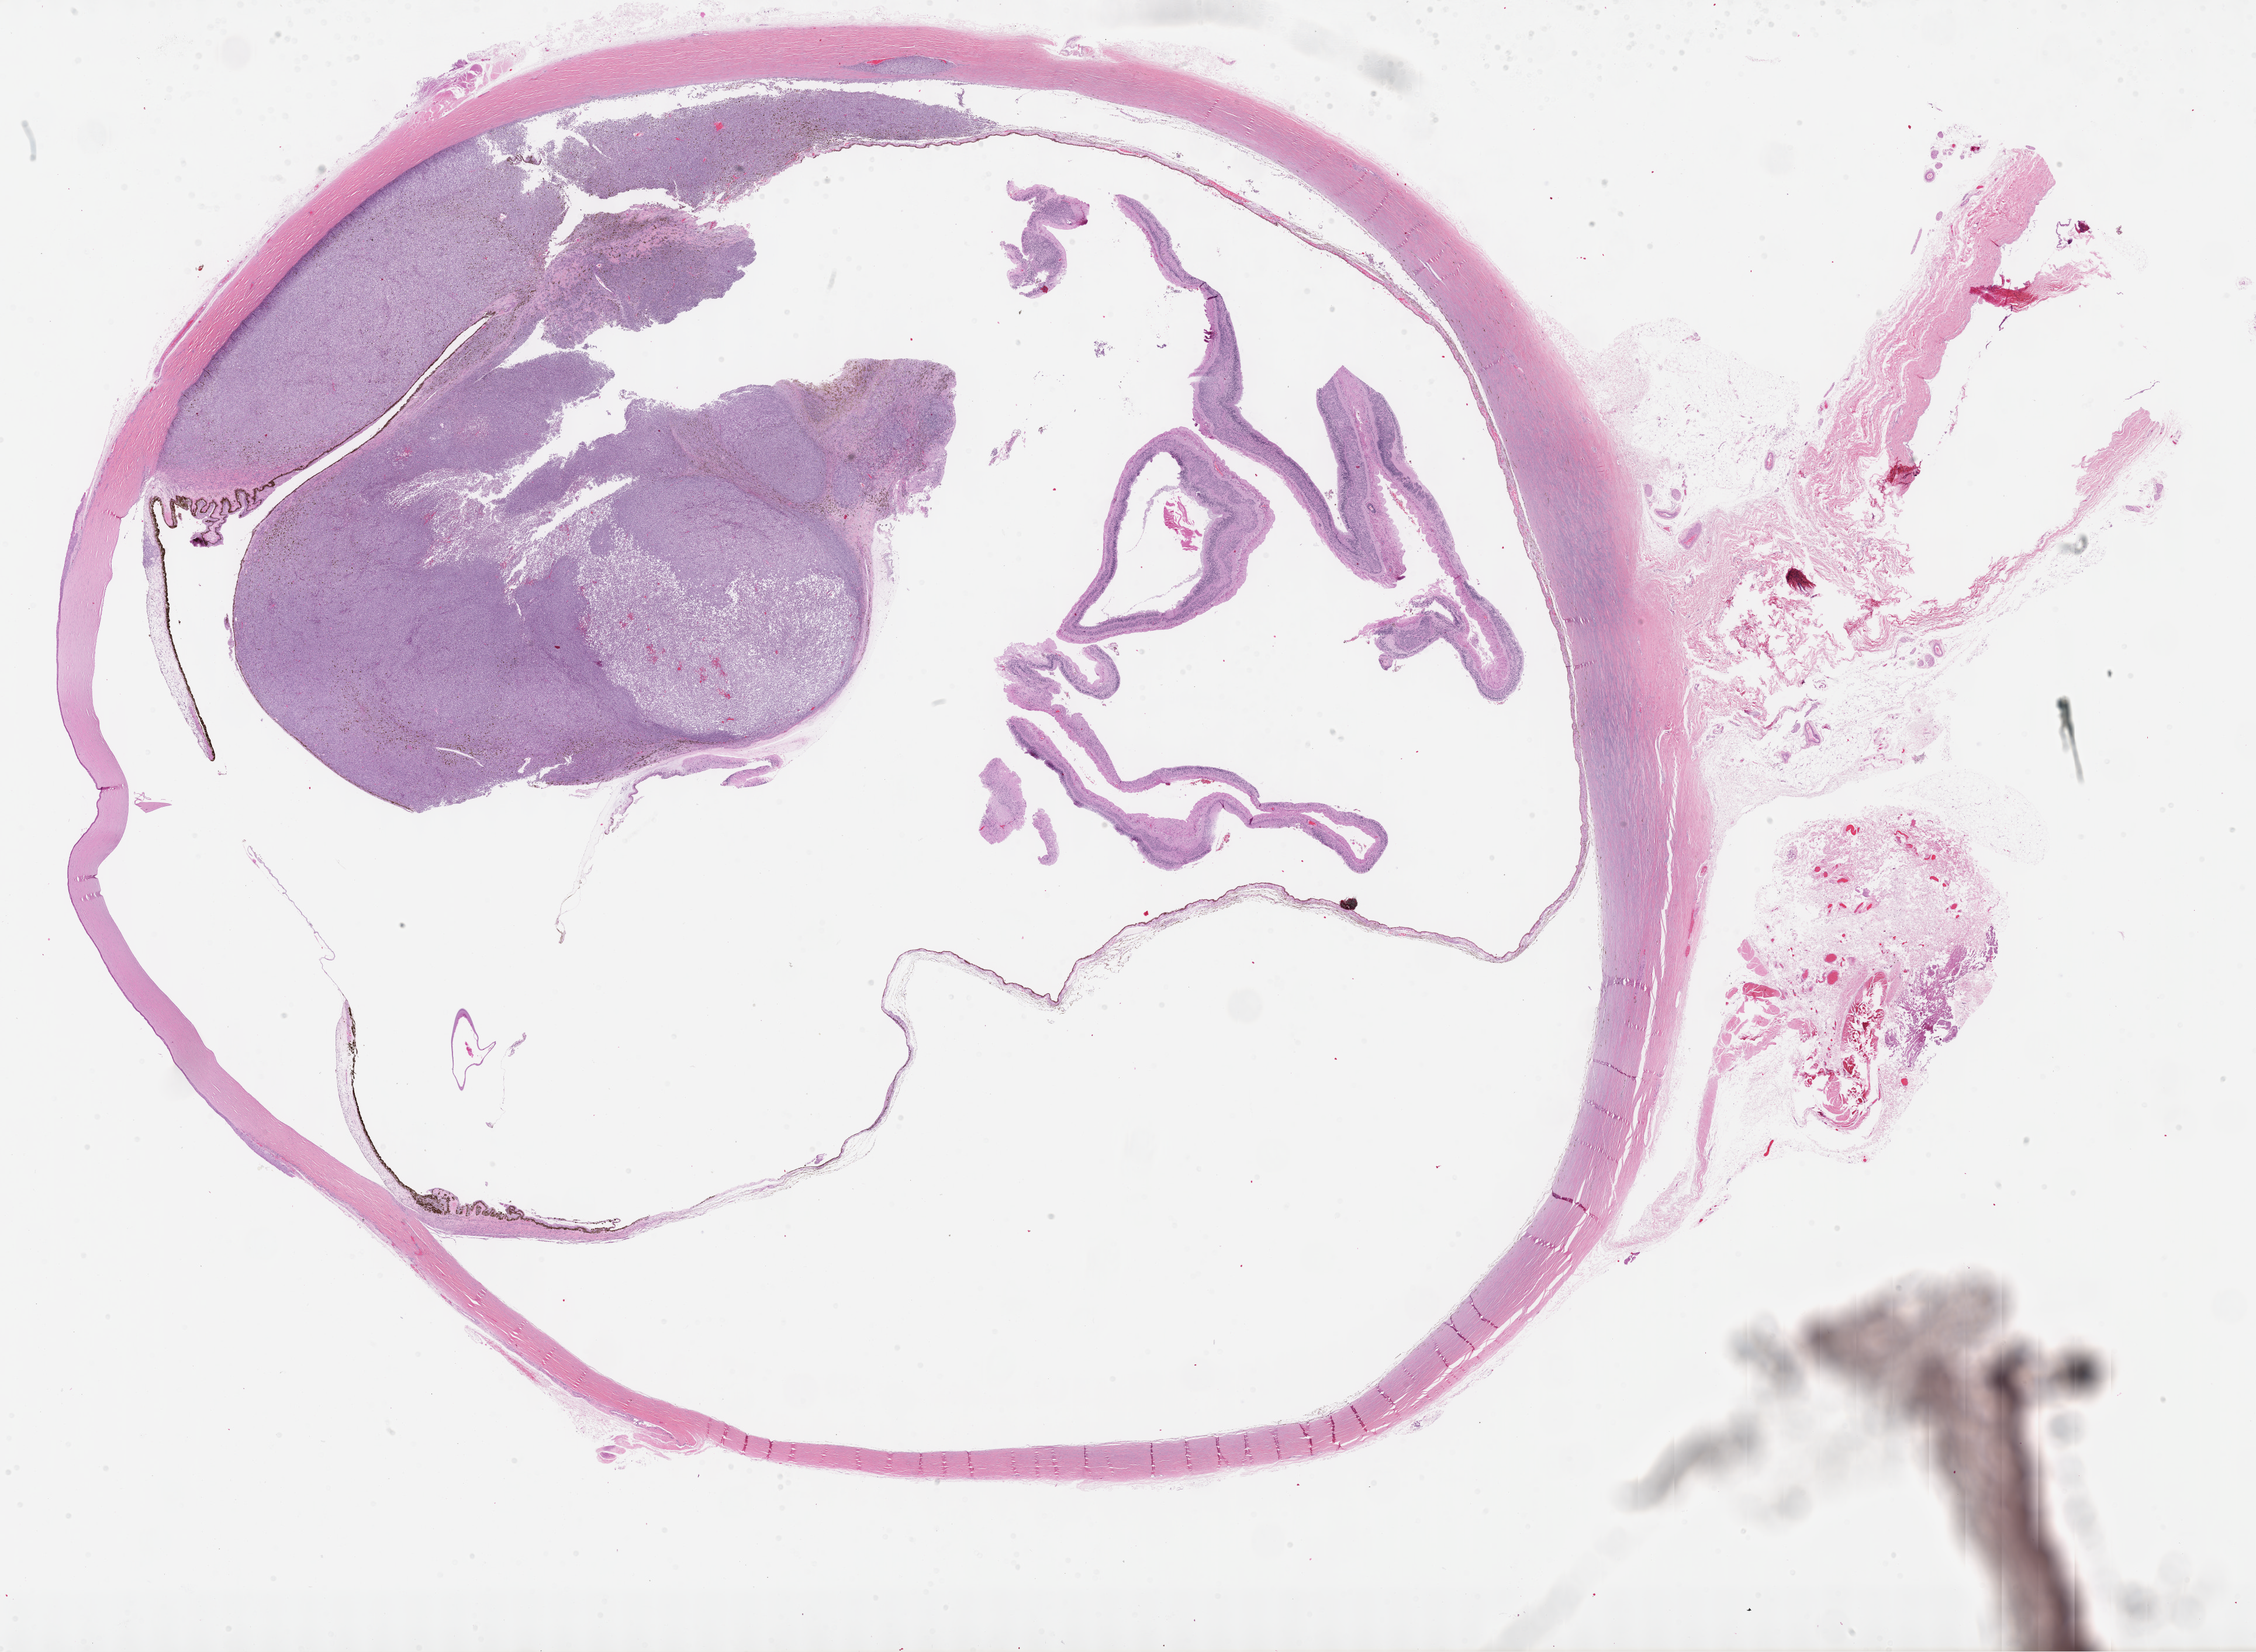
Digitized H&E tissue section (whole slide) — shown as a low-resolution overview of the whole scanned area (about 31.2 x 22.9 mm, acquisition: 40x scan); formalin-fixed paraffin-embedded (FFPE) diagnostic section; primary tumour sample from the uvea. Female, age 35 years at initial diagnosis.
AJCC pathologic stage: IIIB (7th edition). TNM: T4b N0 M0. Diagnosis: Mixed epithelioid and spindle cell melanoma (overlapping lesion of eye and adnexa).